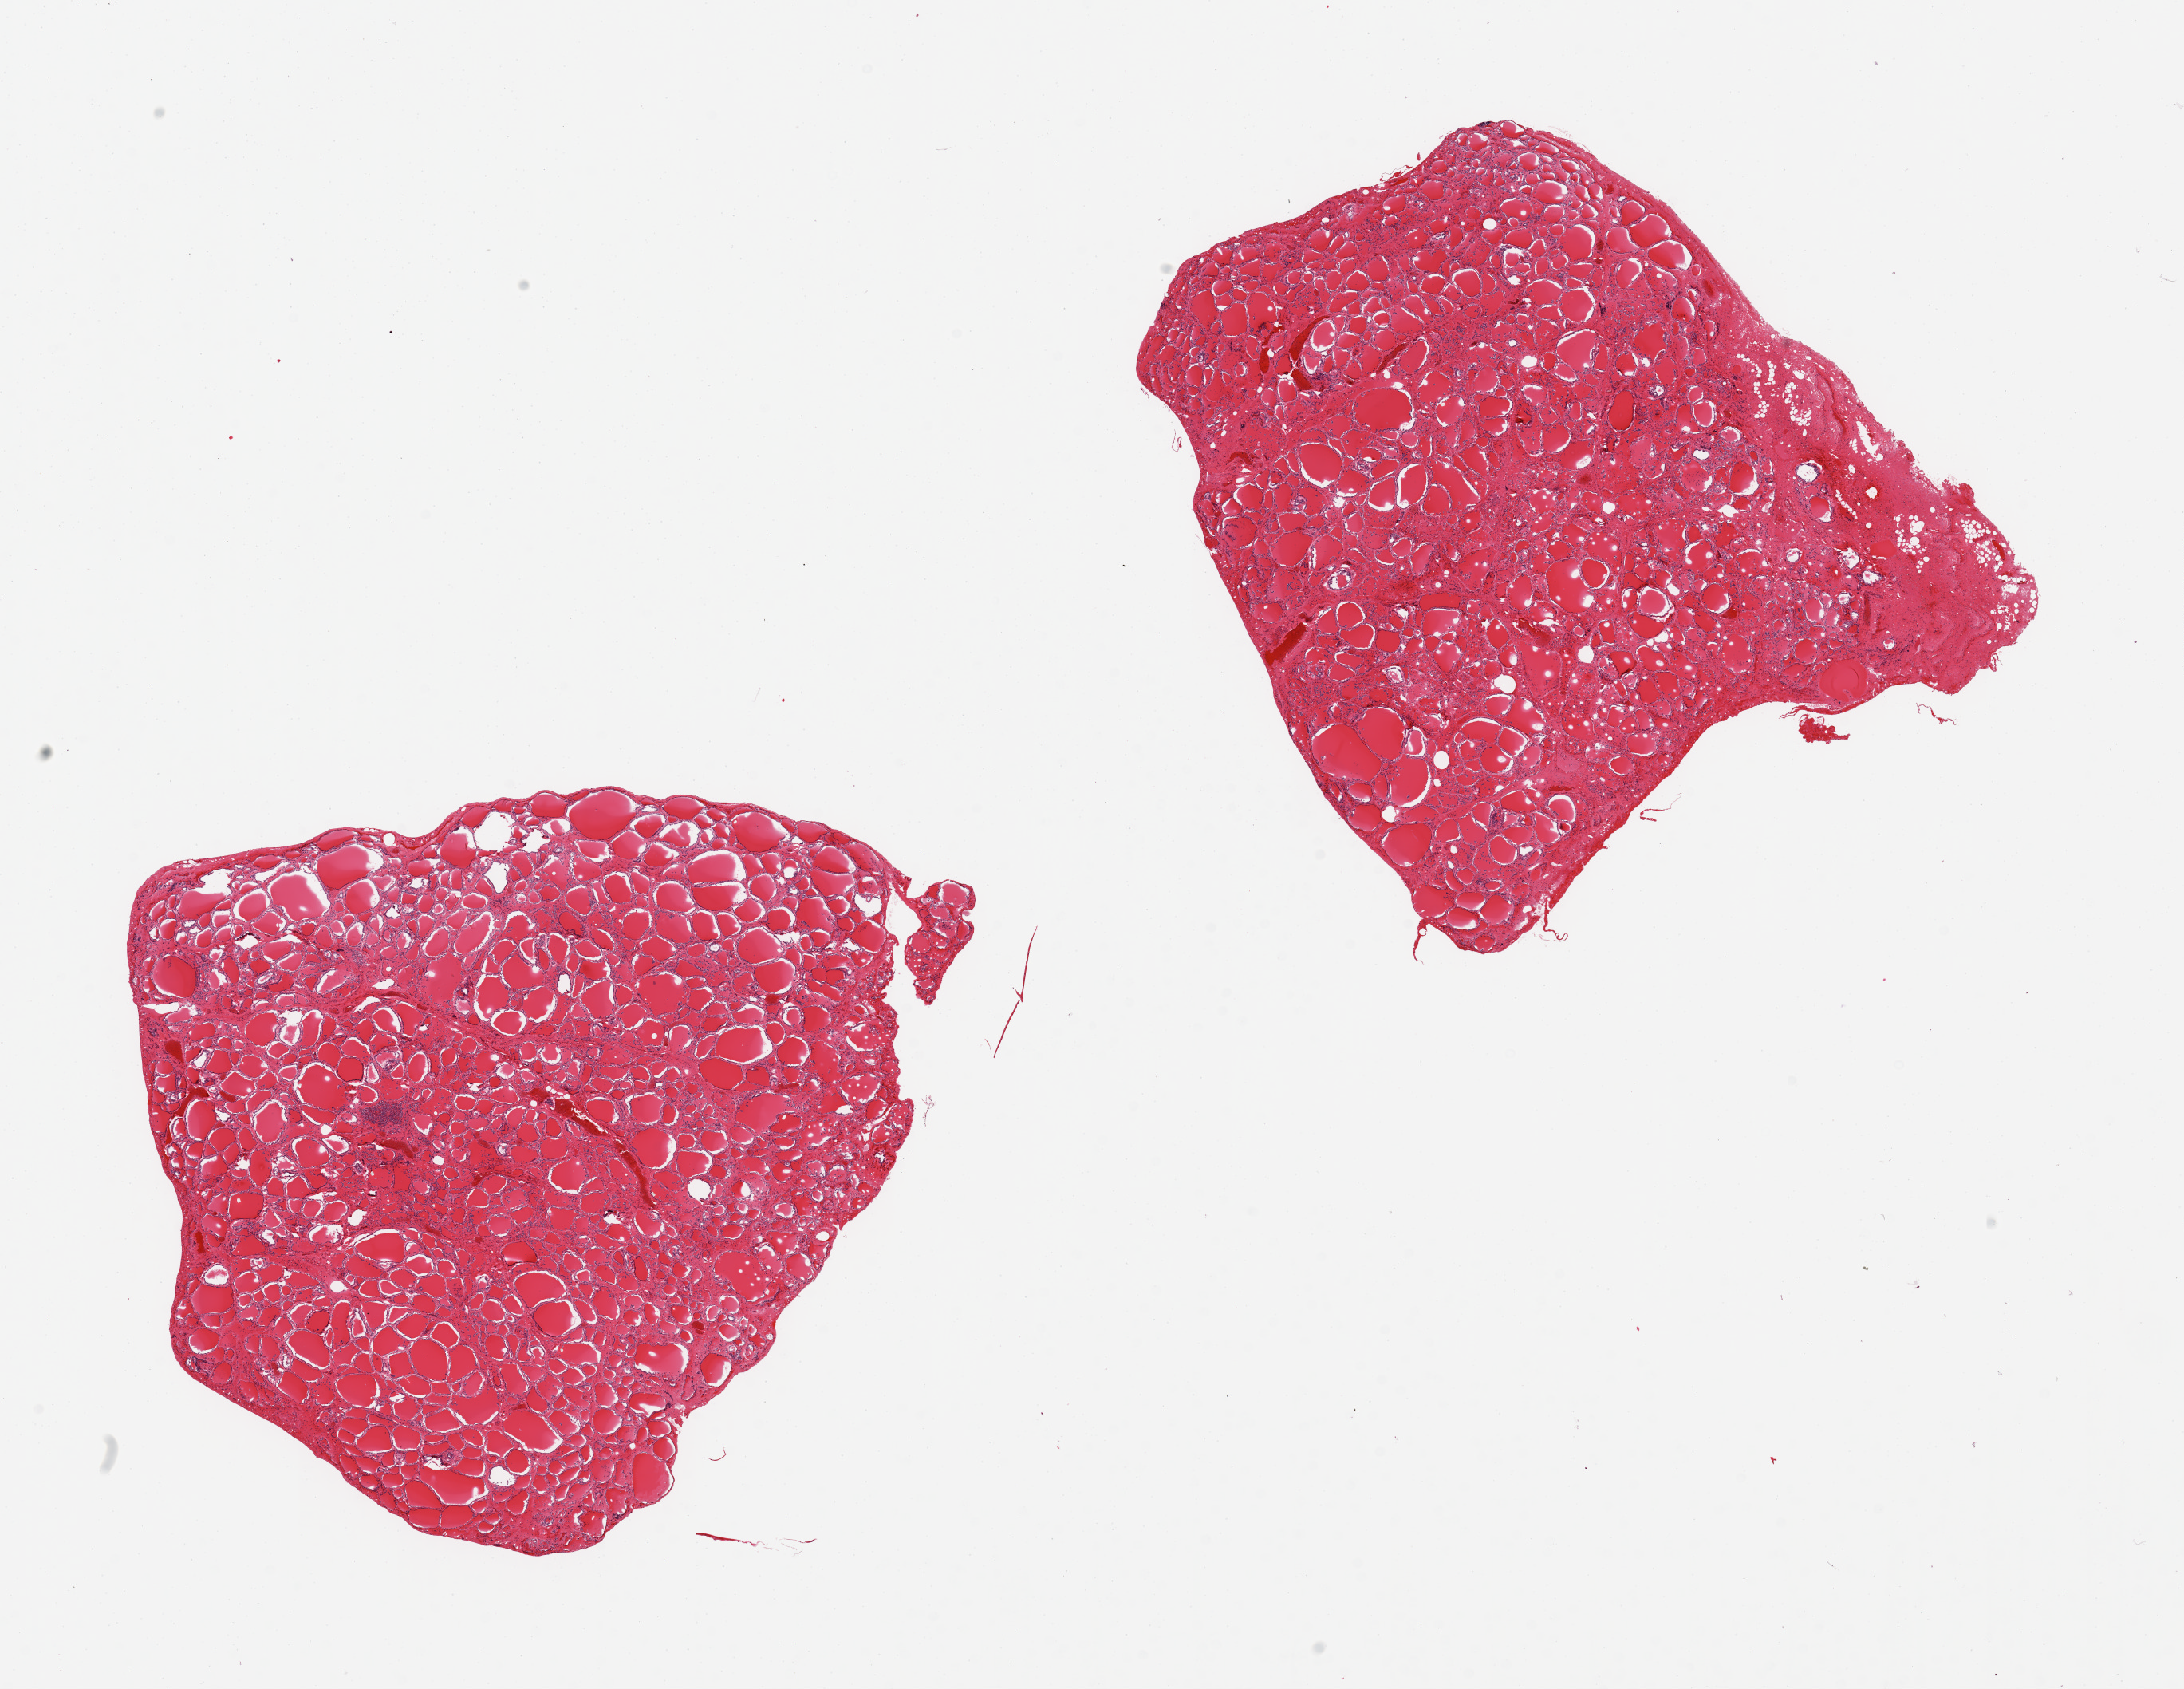
H&E whole-slide image, shown as a low-resolution overview of the whole scanned area (about 21.7 x 16.7 mm, acquisition: 20x scan), PAXgene-fixed, paraffin-embedded tissue, sampled site (target tissue): thyroid, donor tissue sample. Male donor.
Review note (as recorded): 2 pieces, one piece is ~10% fibrovascular and adipose tissue.